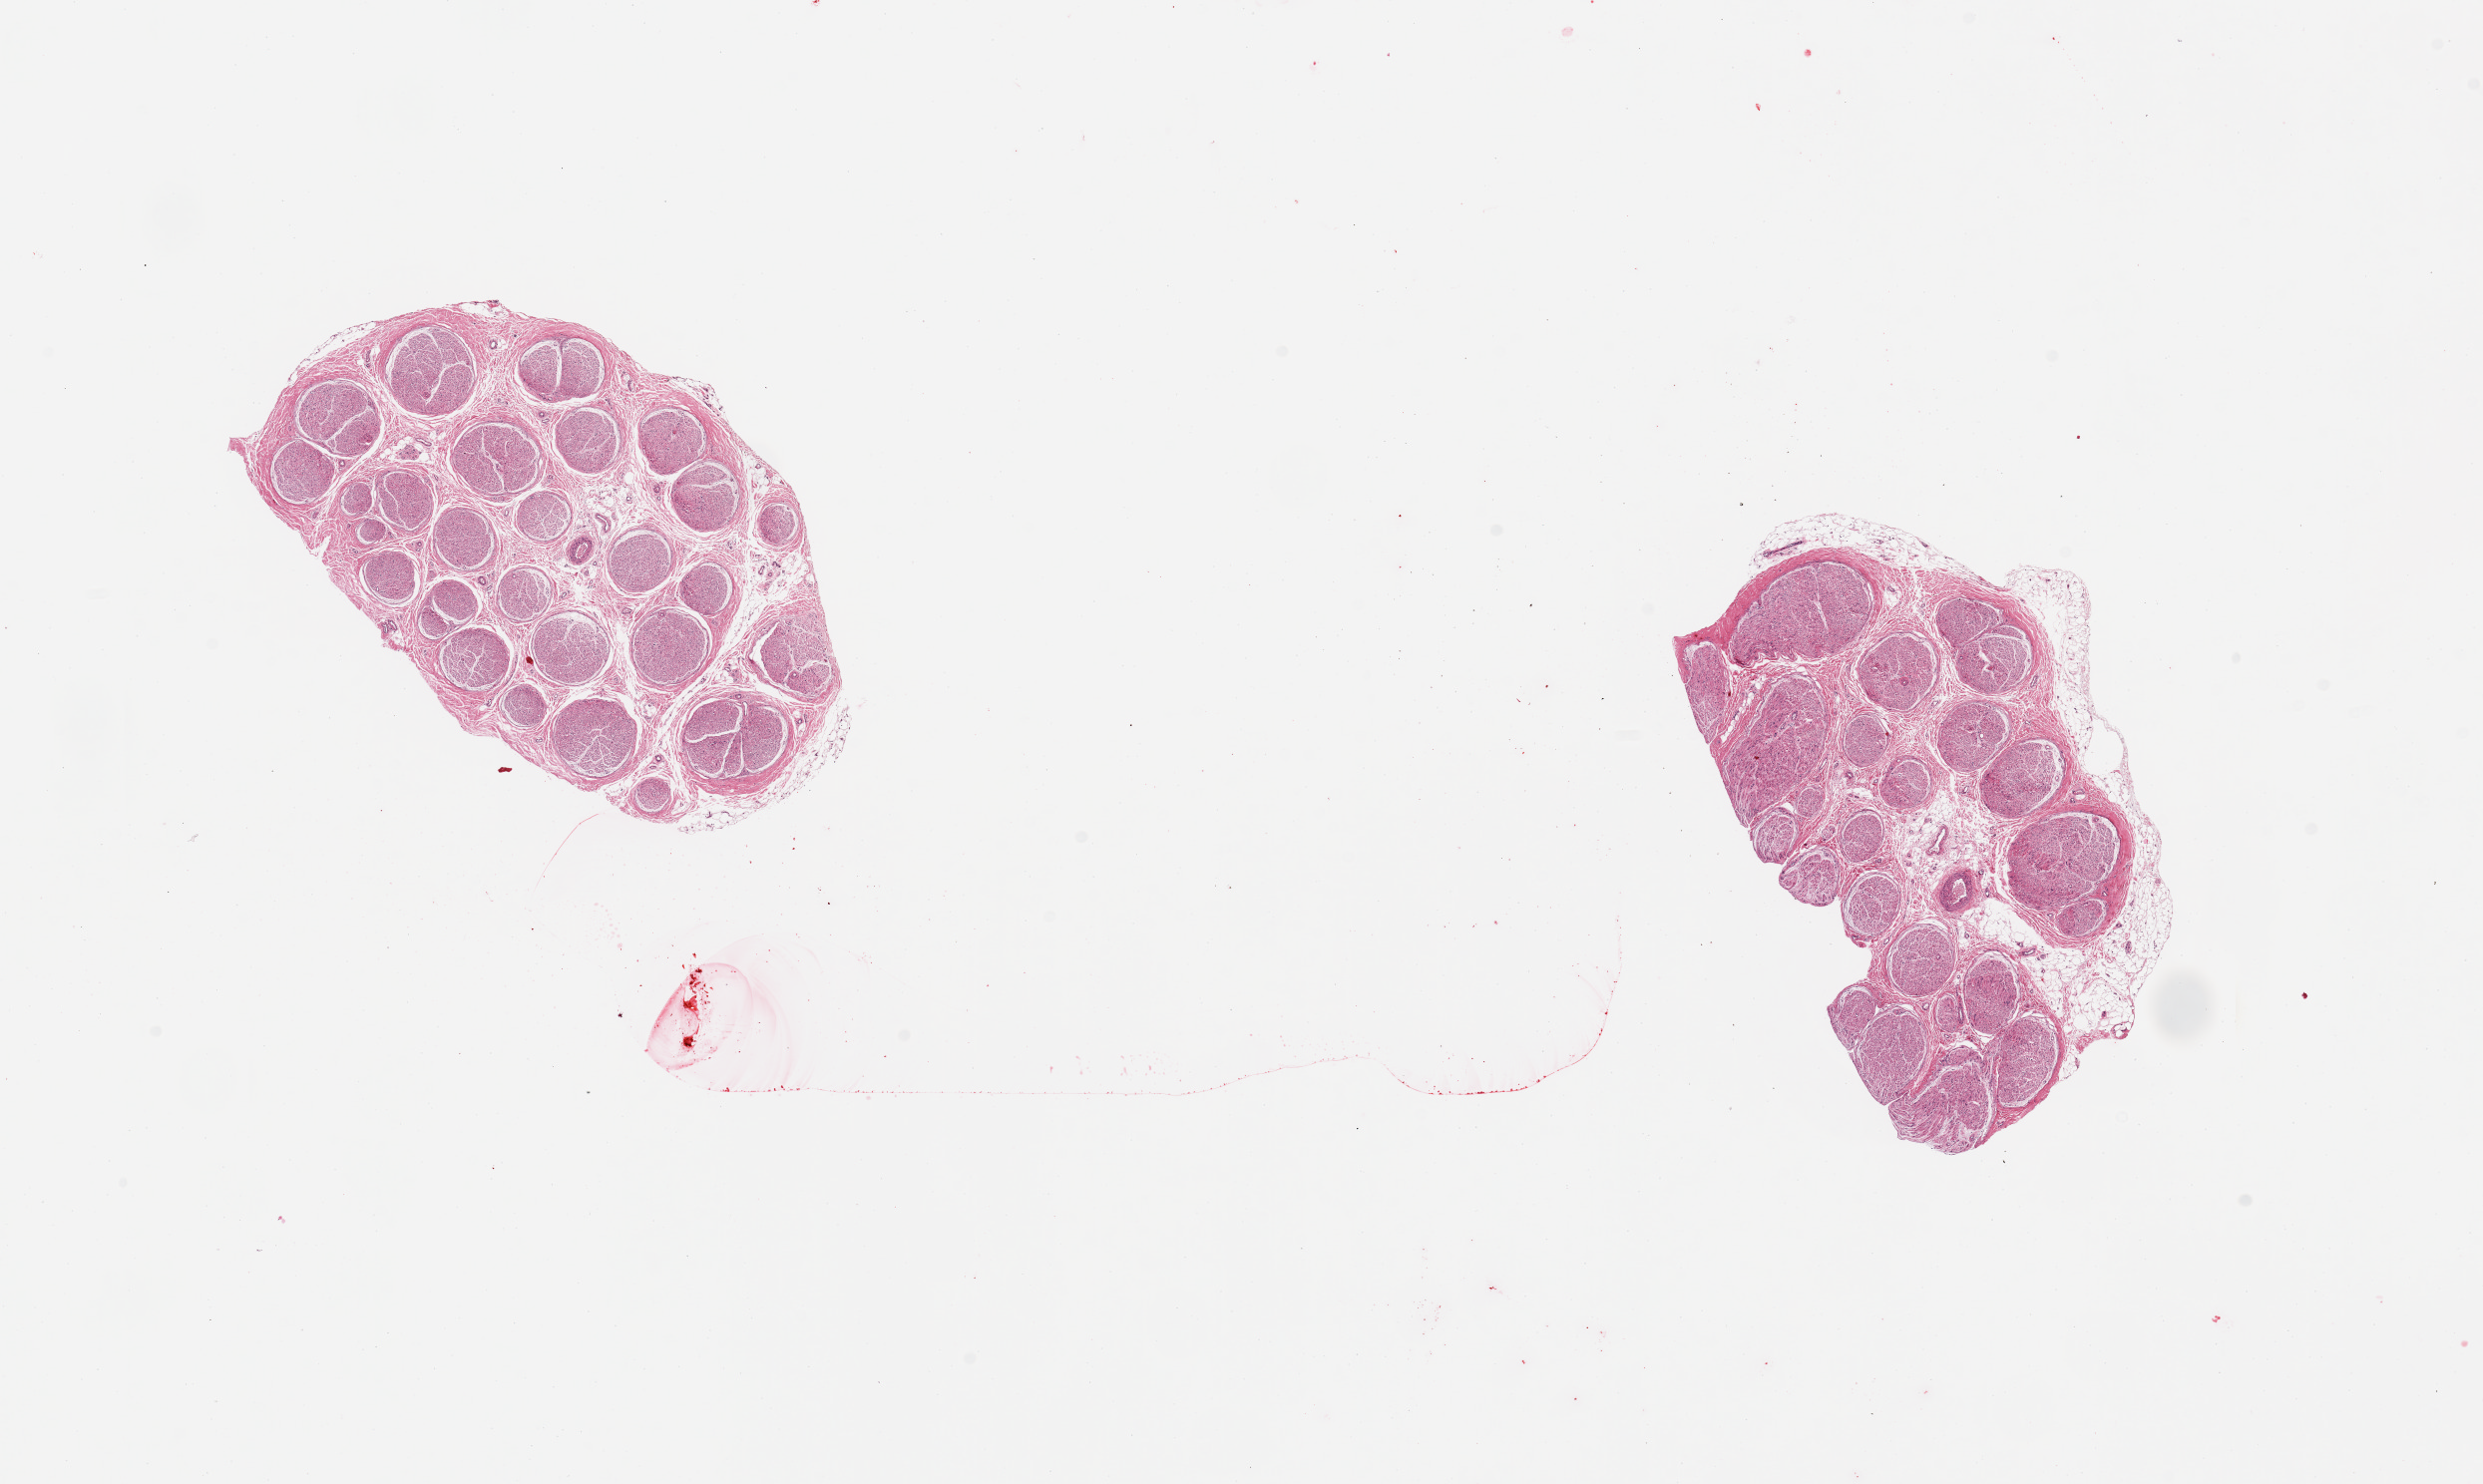
Whole-slide image, H&E stain, a low-resolution overview of the entire scanned area, about 19.7 x 11.8 mm, PAXgene-fixed, paraffin-embedded tissue, target tissue: tibial nerve, tissue donor sample. Donor sex: male.
Reviewer comment on this tissue sample: 2 pieces; 10% fat in 1 piece.